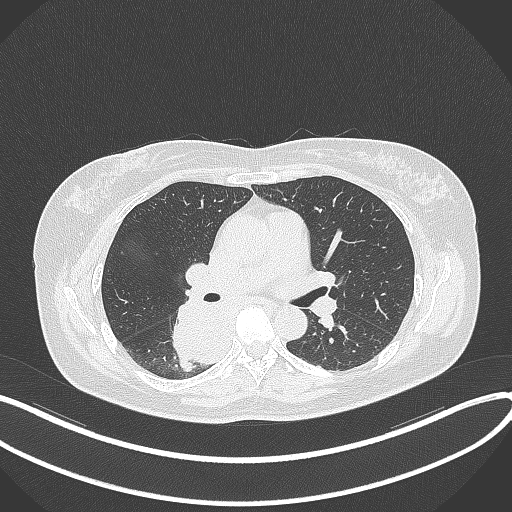
Chest CT, one axial slice; slice 207 of 331 in the series (ordered by position); reconstruction kernel B70f; lung window (W 1500 / L -600 HU); 1 mm slice thickness; 512 × 512 image matrix, field of view 400 × 400 mm. Female patient, age 54 years. Case-level facts recorded for this patient, not image findings: clinical TNM (as recorded): T4 N0 M0.
Annotated regions visible in this slice (bounding box drawn by a radiologist):
- lung tumour (recorded histology: adenocarcinoma): bounding box (x1, y1, x2, y2) in pixels: (164, 302, 233, 368)